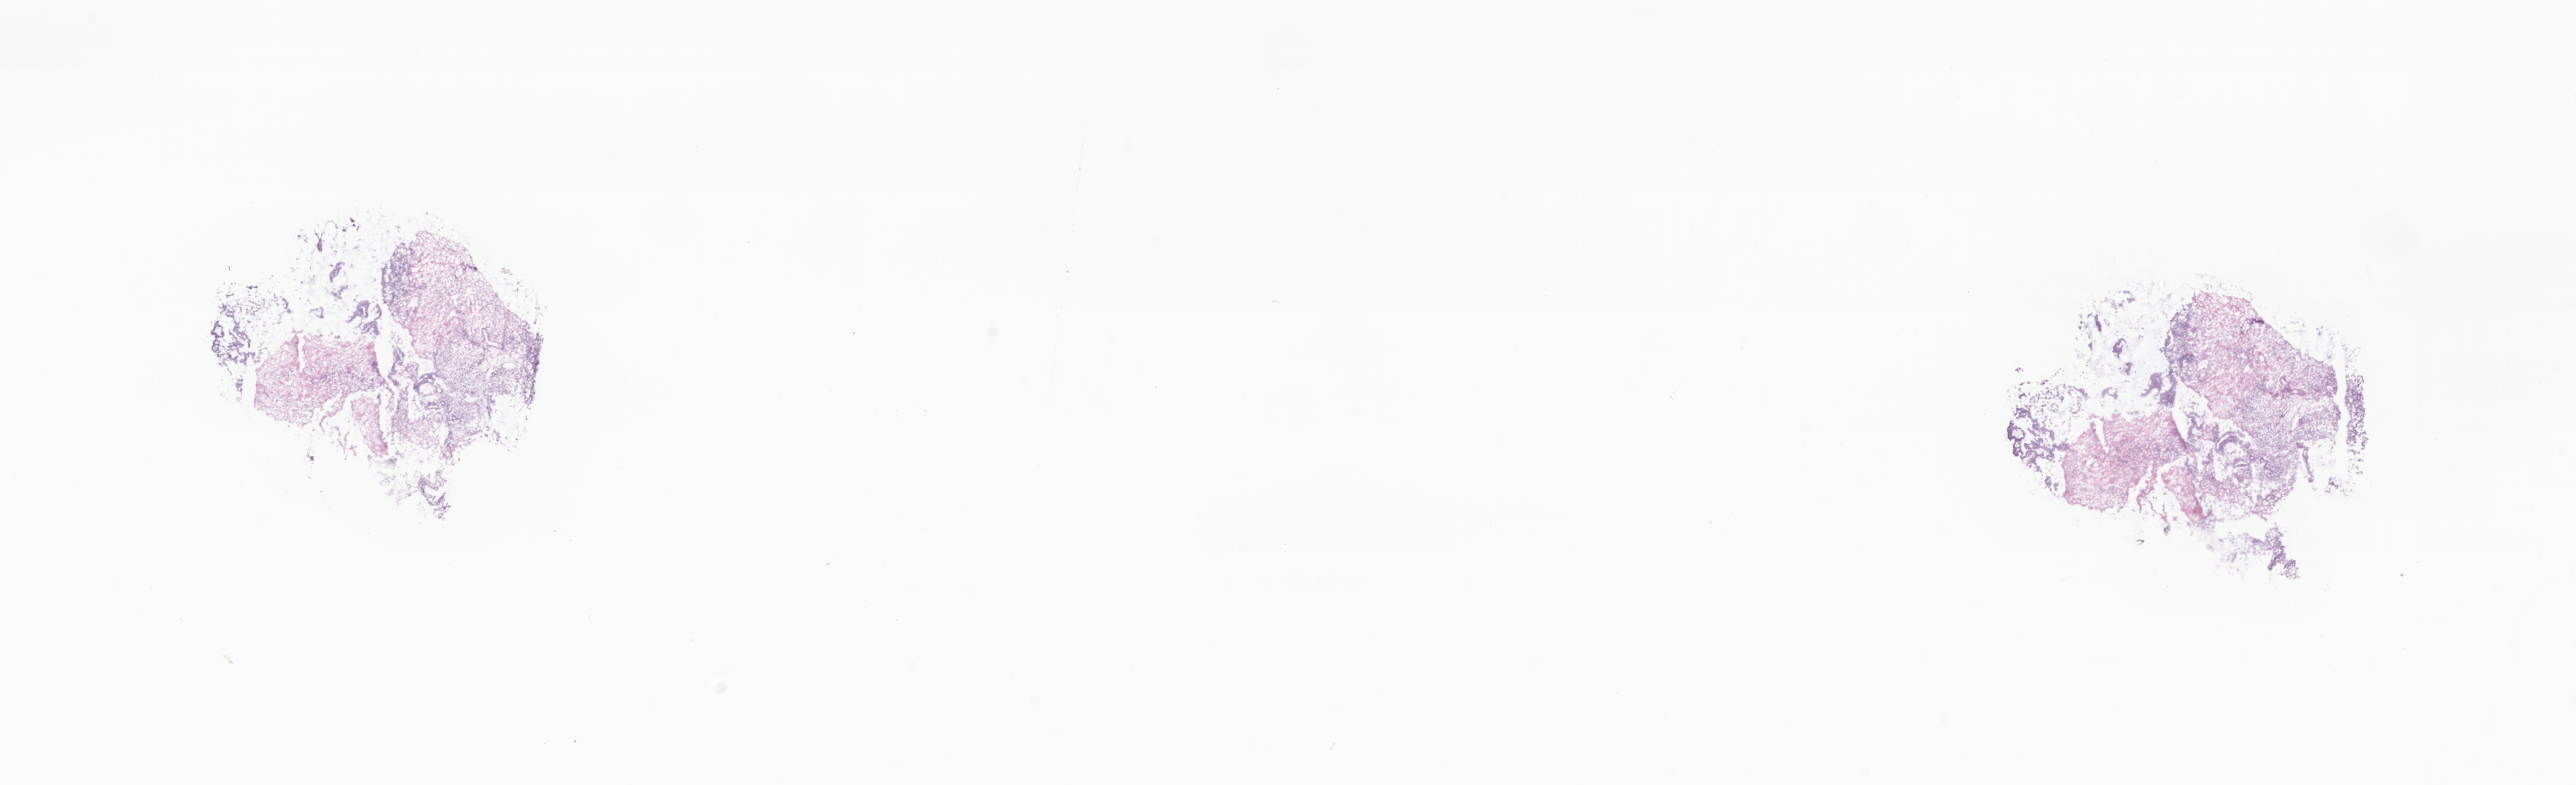
Digitized haematoxylin and eosin-stained section, a low-resolution overview of the entire scanned area, about 22.9 x 7.0 mm. Frozen section (tissue freezing medium). Primary tumor. Anatomic site: ascending colon. Male patient; age at initial diagnosis 75 years. Composition of this section per pathologist review: tumor cells 70%, tumor nuclei 70%, stromal cells 30%, necrosis 0%, normal cells 0%. Inflammatory infiltration, as recorded: lymphocyte infiltration 4%, monocyte infiltration 3%, neutrophil infiltration 7%.
- section: bottom of the tissue portion
- histologic diagnosis: Adenocarcinoma, NOS